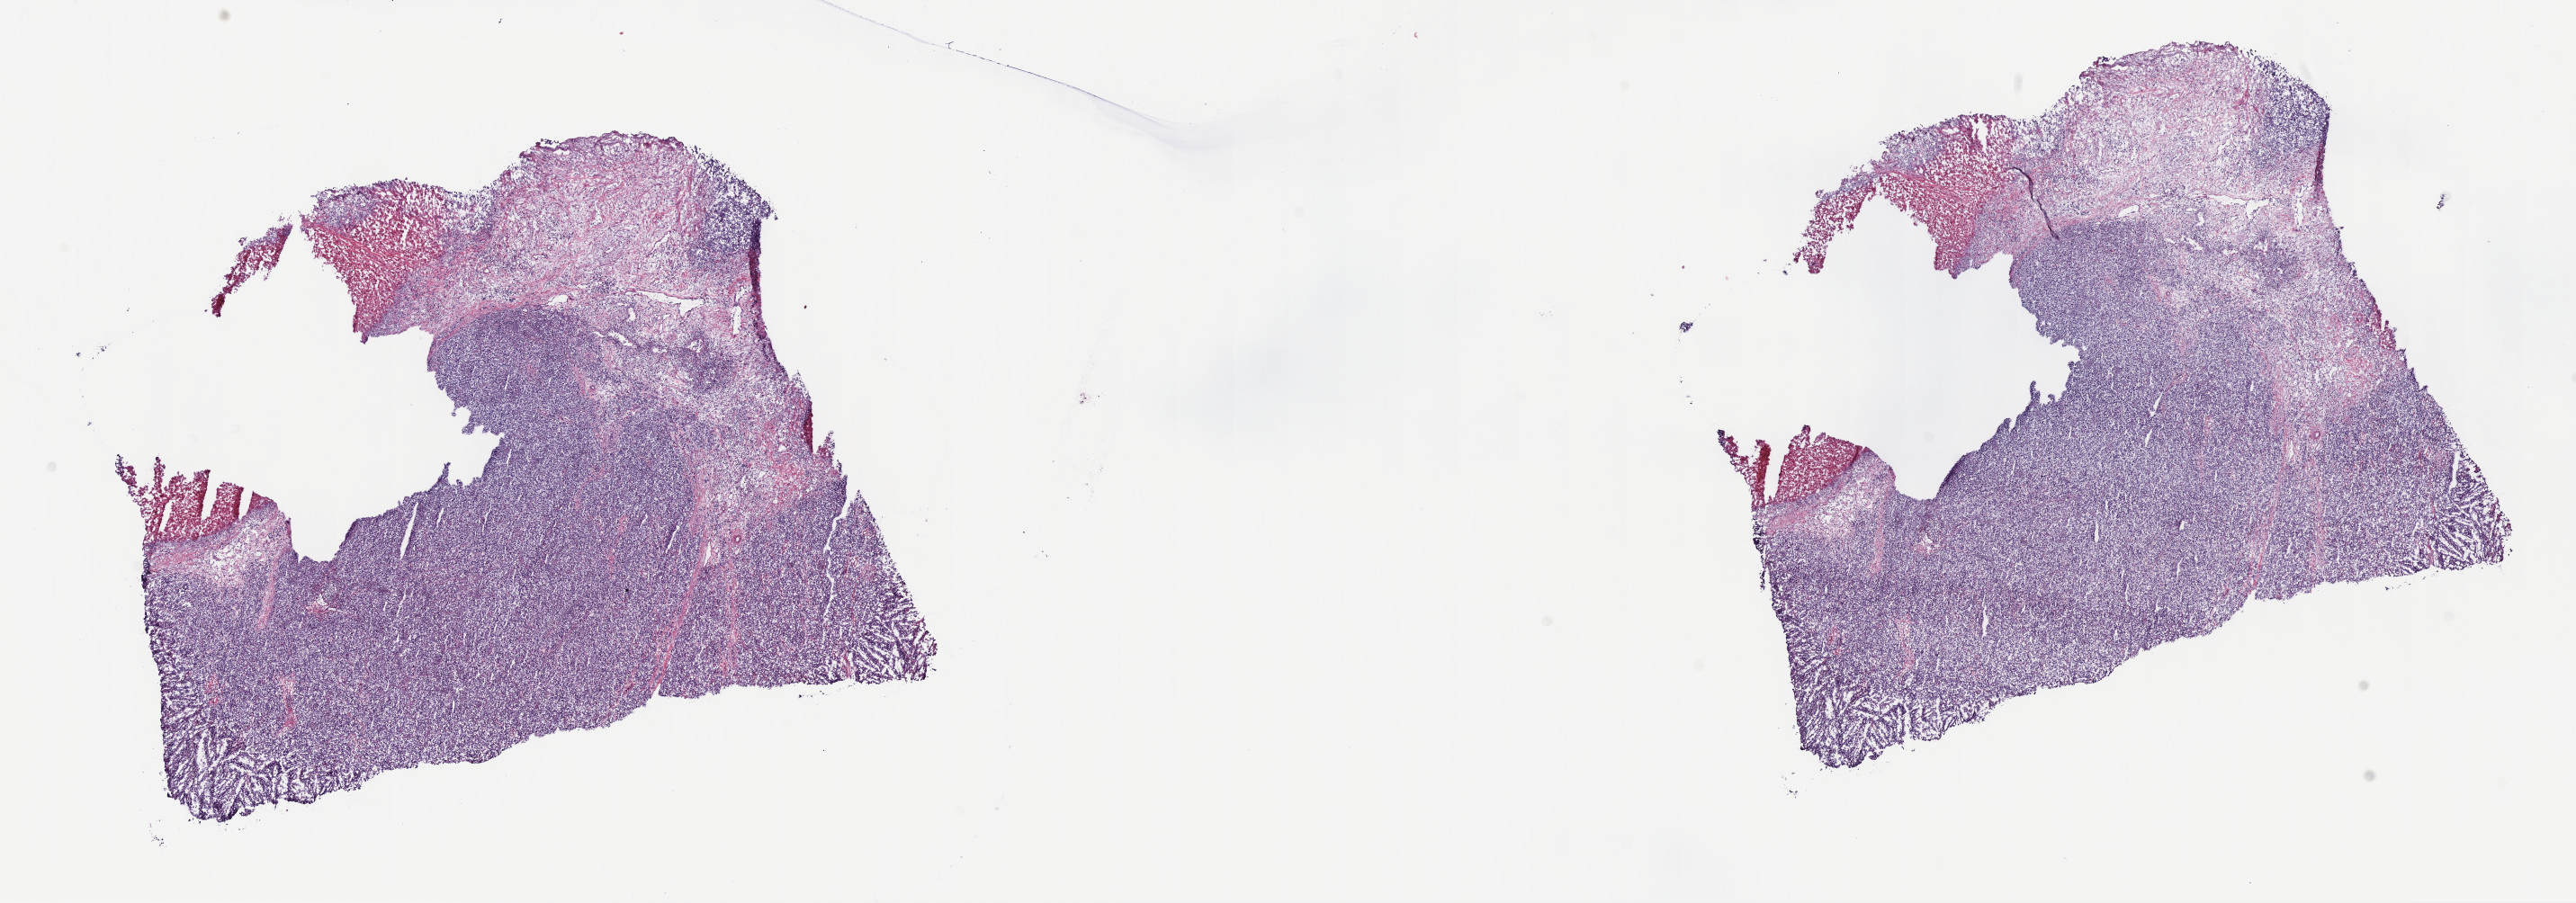
Digitized Hematoxylin and eosin (H&E) stained tissue section (whole slide) — low-resolution overview of the scanned area, about 23.2 x 8.1 mm, frozen section from the top of the tissue portion, primary tumour sample from the testis. Male, age 30 years at initial diagnosis. Composition of this section per pathologist review: tumour cells 93%, tumour nuclei 80%, normal cells 0%, stromal cells 0%, necrosis 7%. Infiltration values recorded for this section: lymphocyte infiltration 3%, monocyte infiltration 0%, neutrophil infiltration 0%.
• AJCC pathologic stage: IS (5th edition)
• diagnosis: Seminoma, NOS